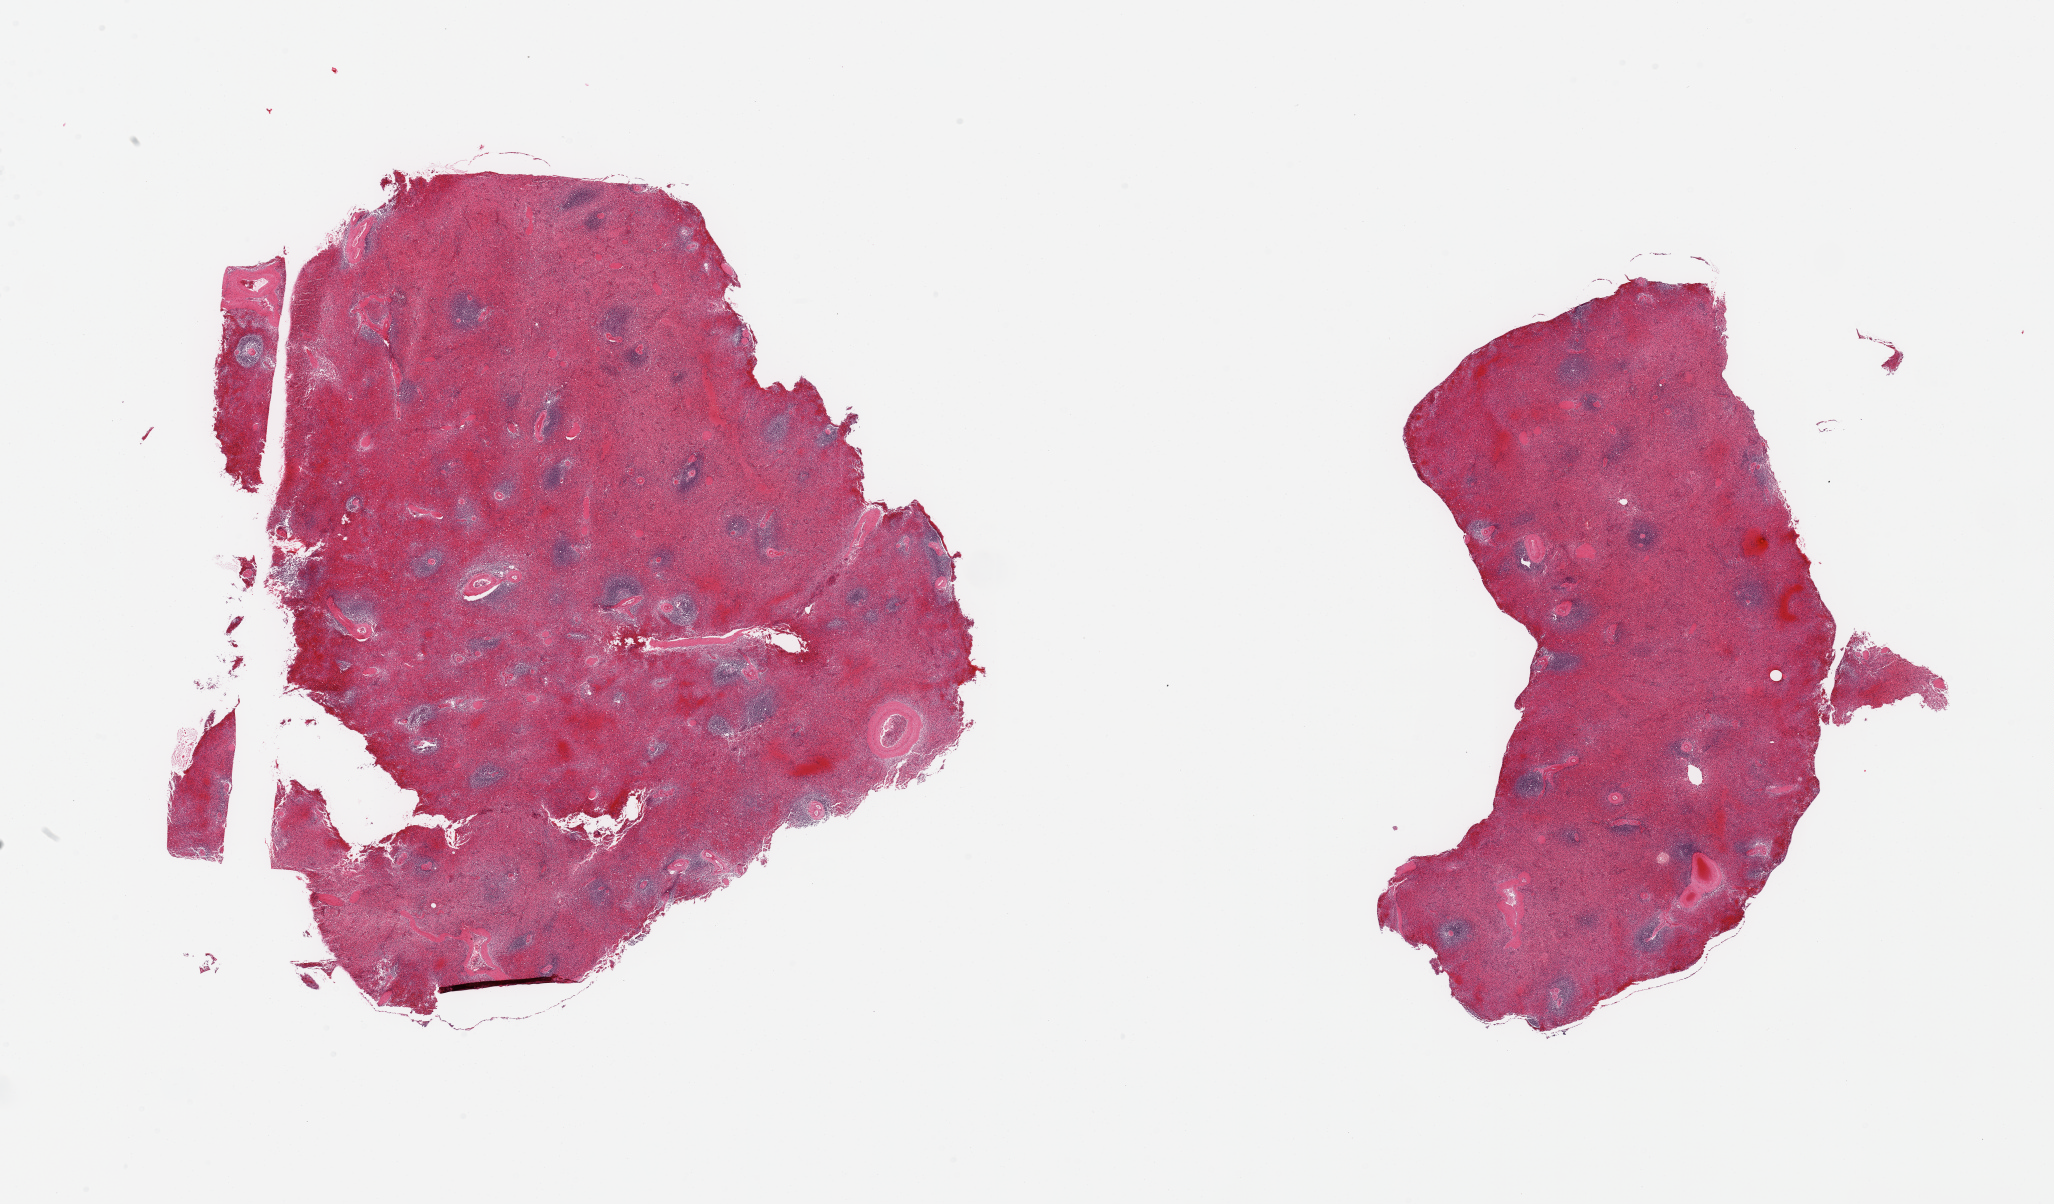
Digitized H&E-stained section — low-resolution overview of the scanned area, about 32.5 x 19.0 mm (from a 20x scan); PAXgene-fixed, paraffin-embedded tissue; target tissue: spleen; donor tissue sample.
Pathologist's review note for this sample: 2 pieces; congestion.